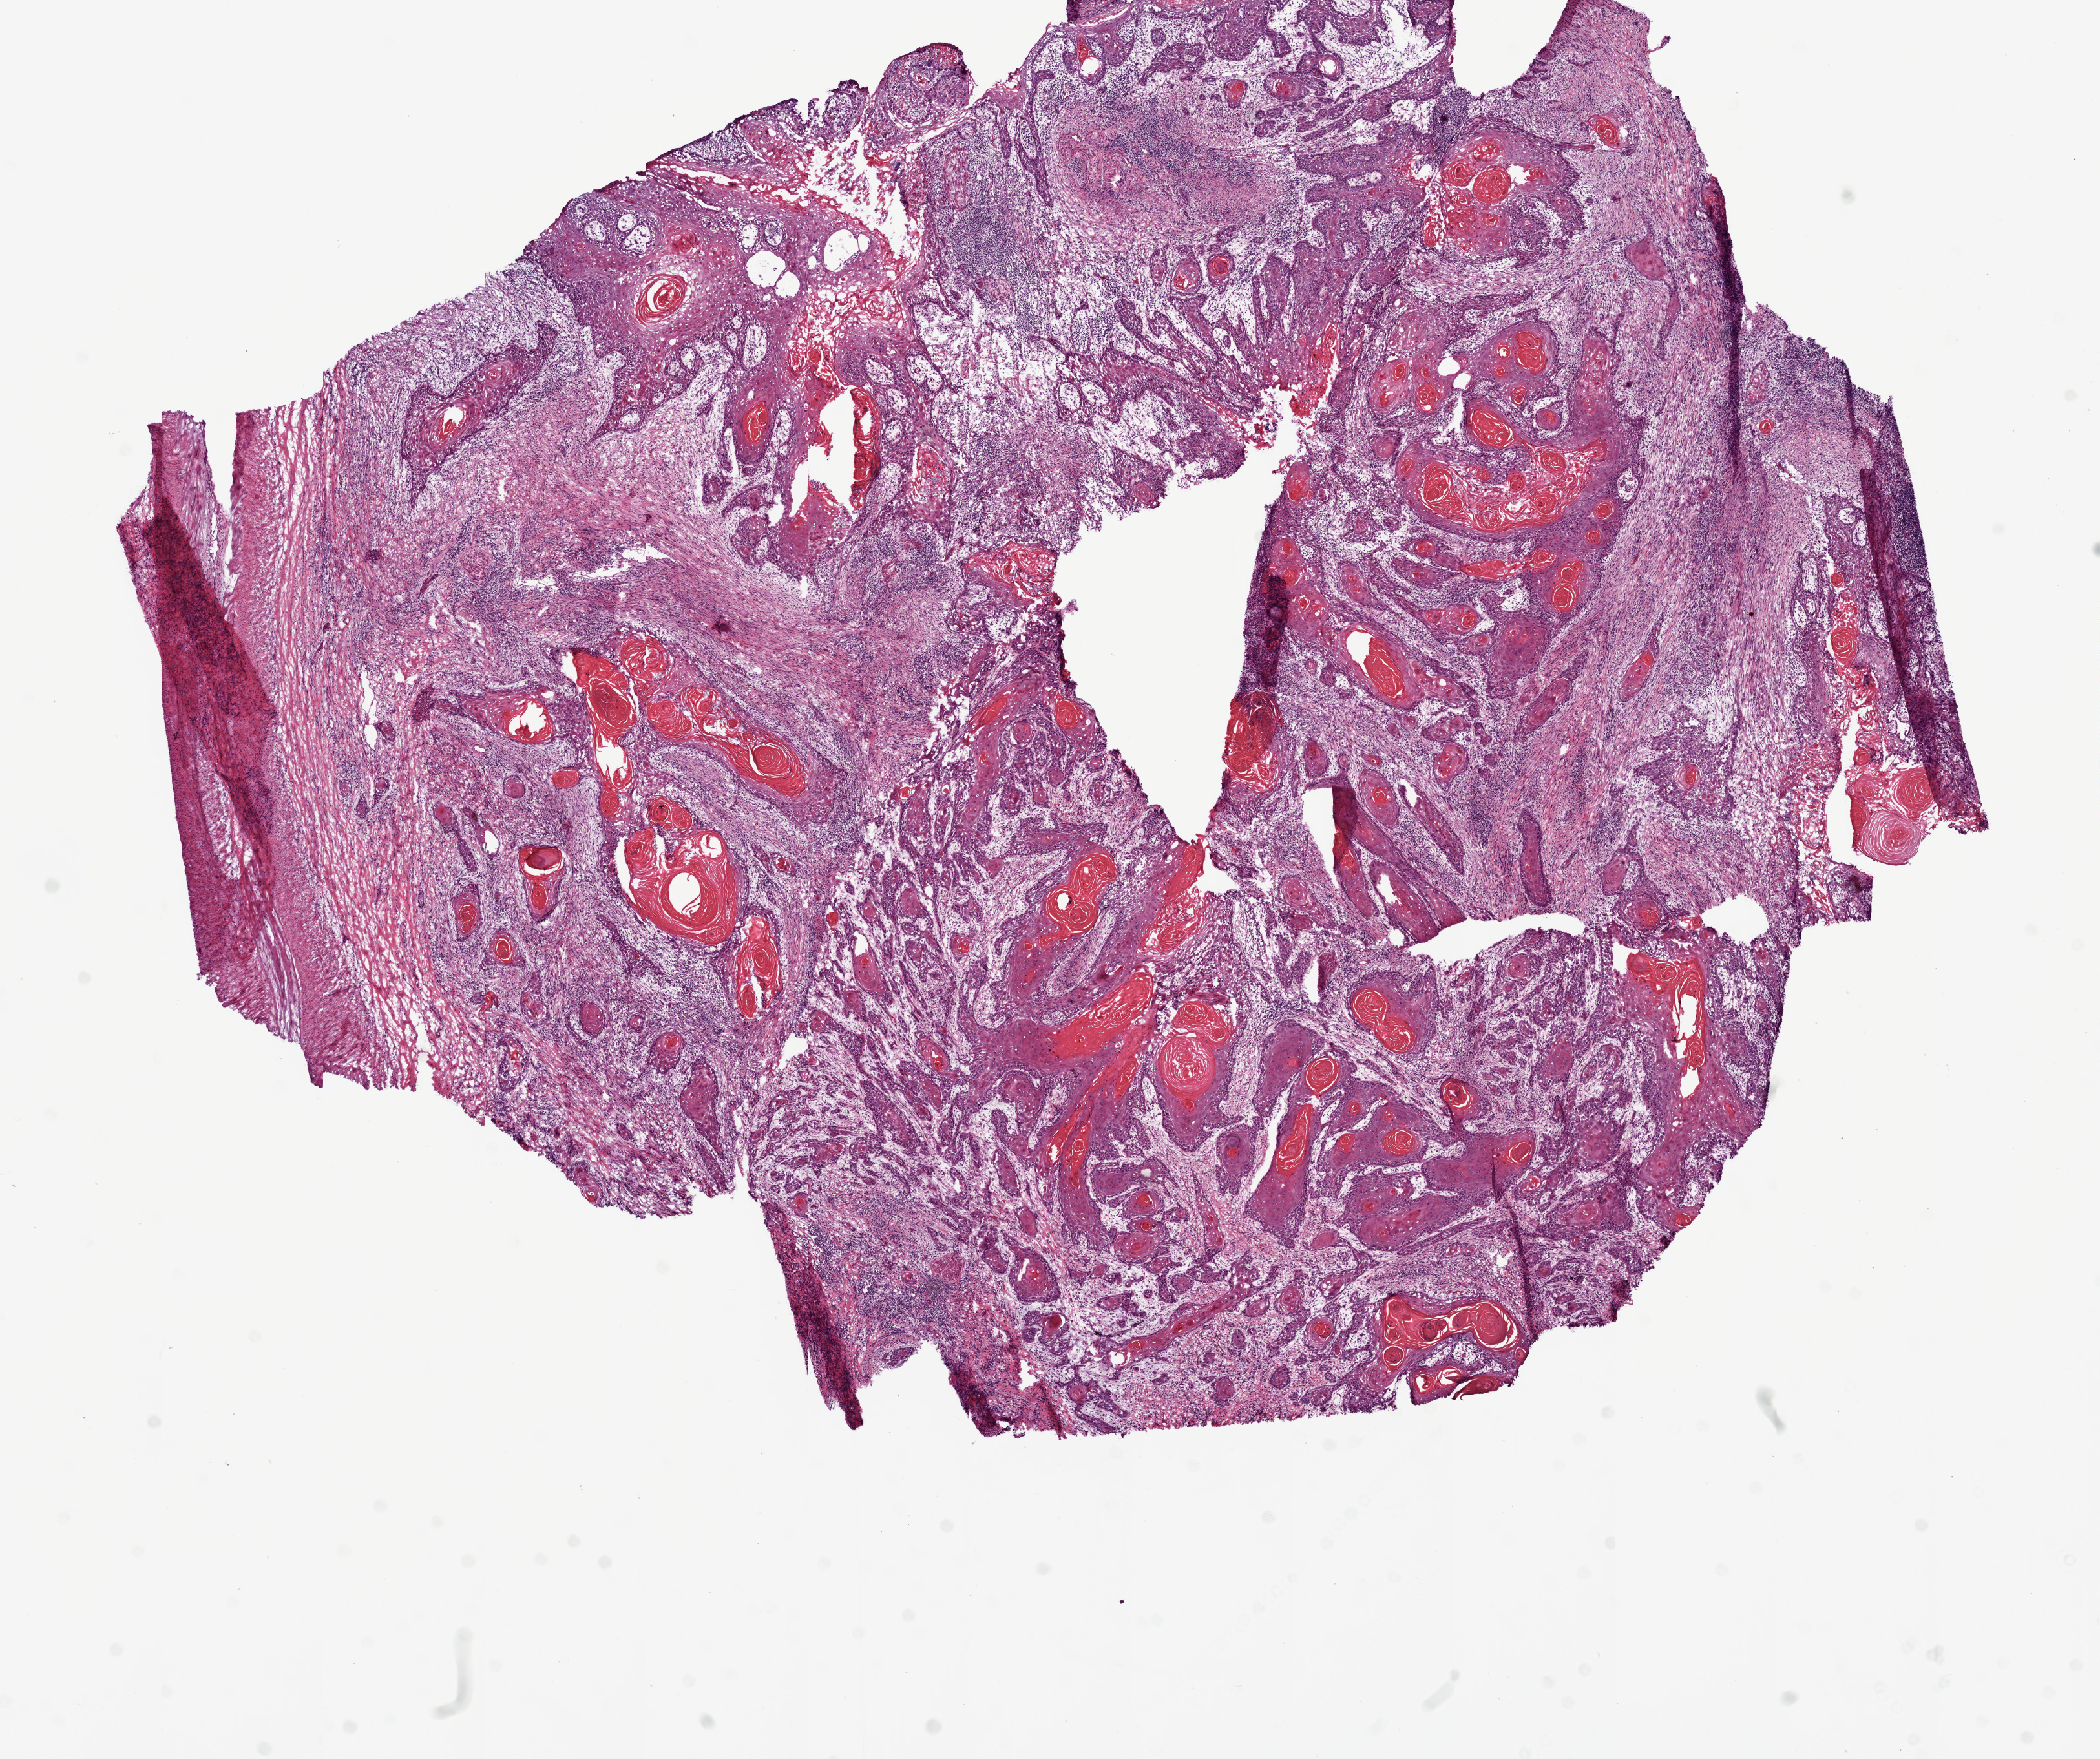
Digitized H&E tissue section (whole slide) — shown as a low-resolution overview of the whole scanned area (about 13.0 x 10.9 mm, slide scanned at 20x), frozen section, primary tumour sample from the head and neck. Female patient; age at initial diagnosis 48 years. Histologic grade: G3 (poorly differentiated). Composition of this section per pathologist review: tumour cells 70%, tumour nuclei 65%, normal cells 0%, stromal cells 30%, necrosis 0%.
AJCC pathologic stage: IVA (6th edition). Histologic diagnosis: Squamous cell carcinoma, NOS (tongue, NOS).